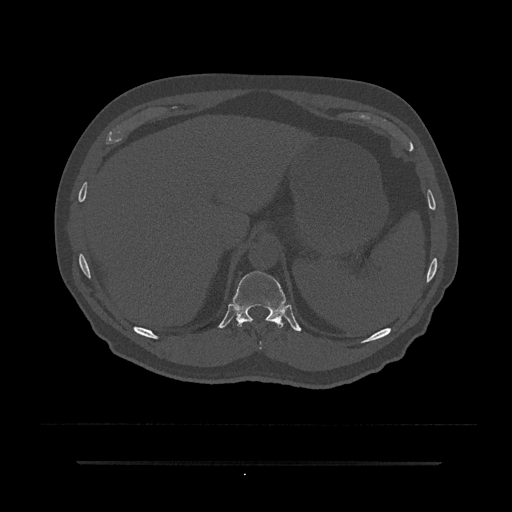
CT including the spine, one axial slice. Slice 287 of 797 in the series (ordered by position). Reconstruction kernel Br40s/3. 120 kVp. Bone window (W 1800 / L 400 HU). 0.5 mm slice thickness. 512 × 512 image matrix, field of view 464 × 464 mm. Male patient, age 59 years. From the clinical record (not read from this slice): primary cancer: bile ducts.
Outlined on this slice (semi-automatically segmented with operator editing):
- T10 vertebra: bounding box <260,341,262,349> (left, top, right, bottom; pixels)
- T11 vertebra: <231,271,289,328>